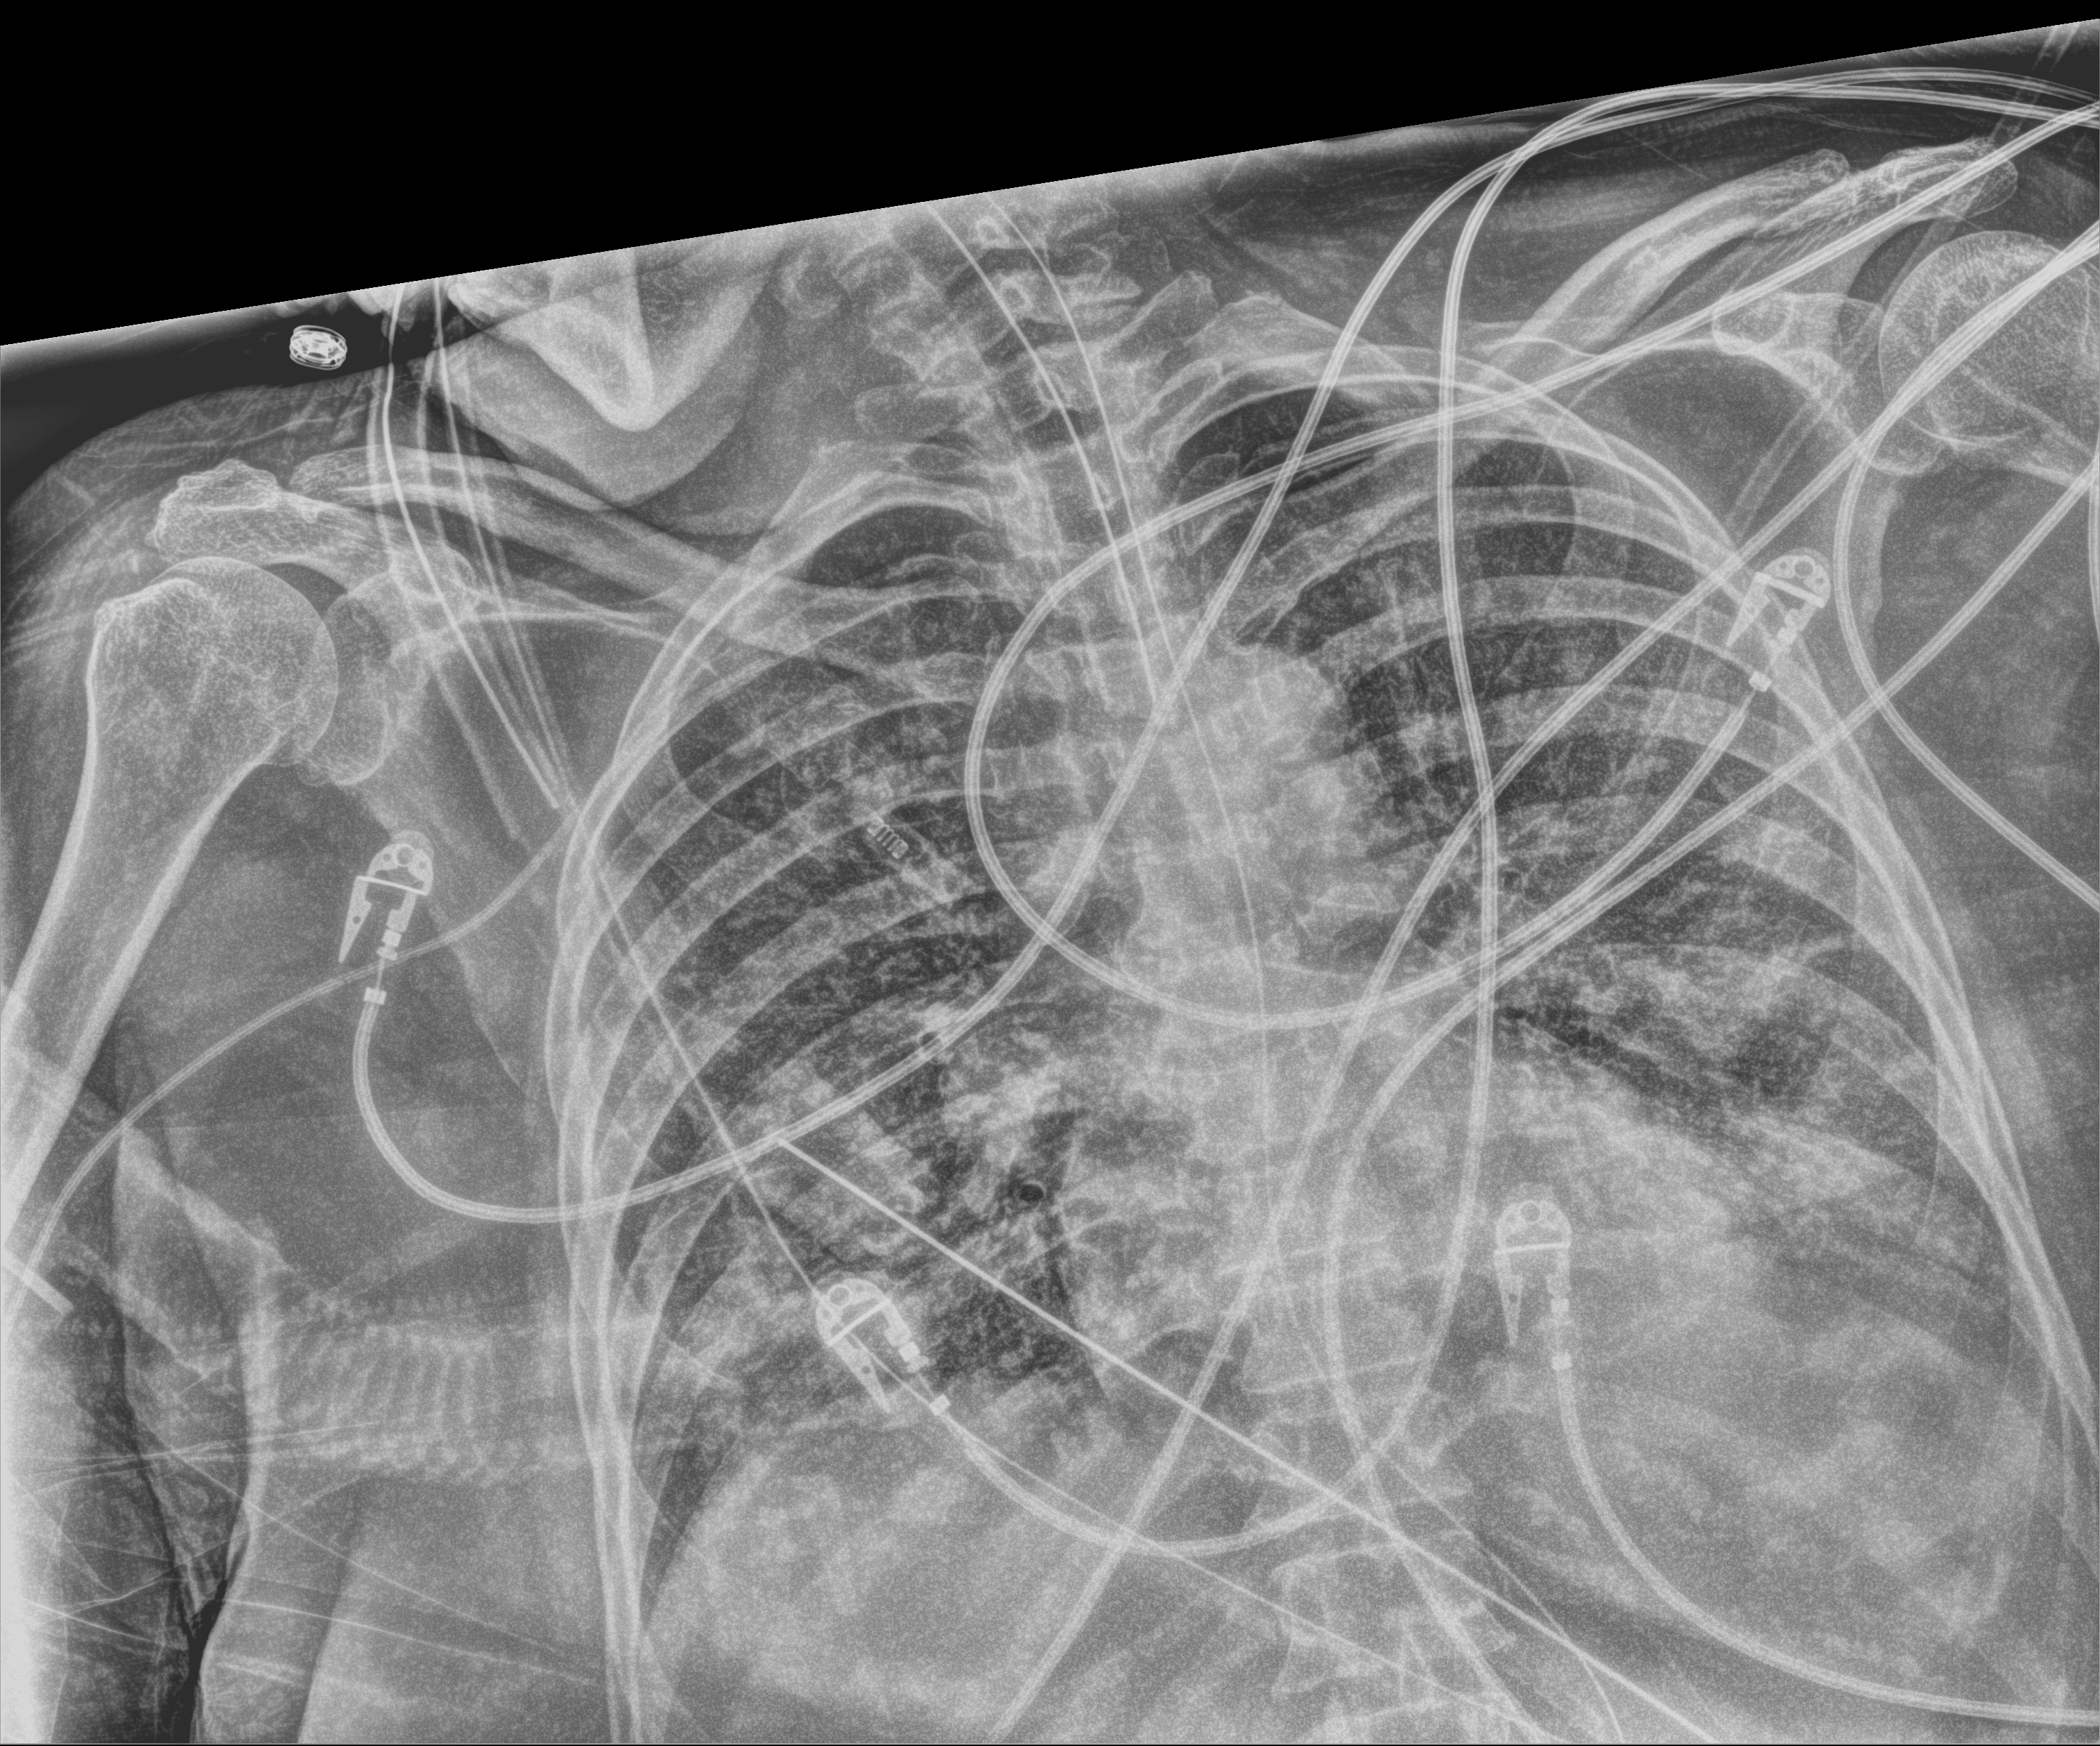
Bedside chest radiograph (computed radiography). Female patient hospitalised with COVID-19, age 75–90 years.
Admission-level facts for this patient (not findings on this image; timing relative to this image not recorded):
- COPD (admission record): no
- length of hospital stay: 26 days
- admitted to intensive care during this hospital stay: yes